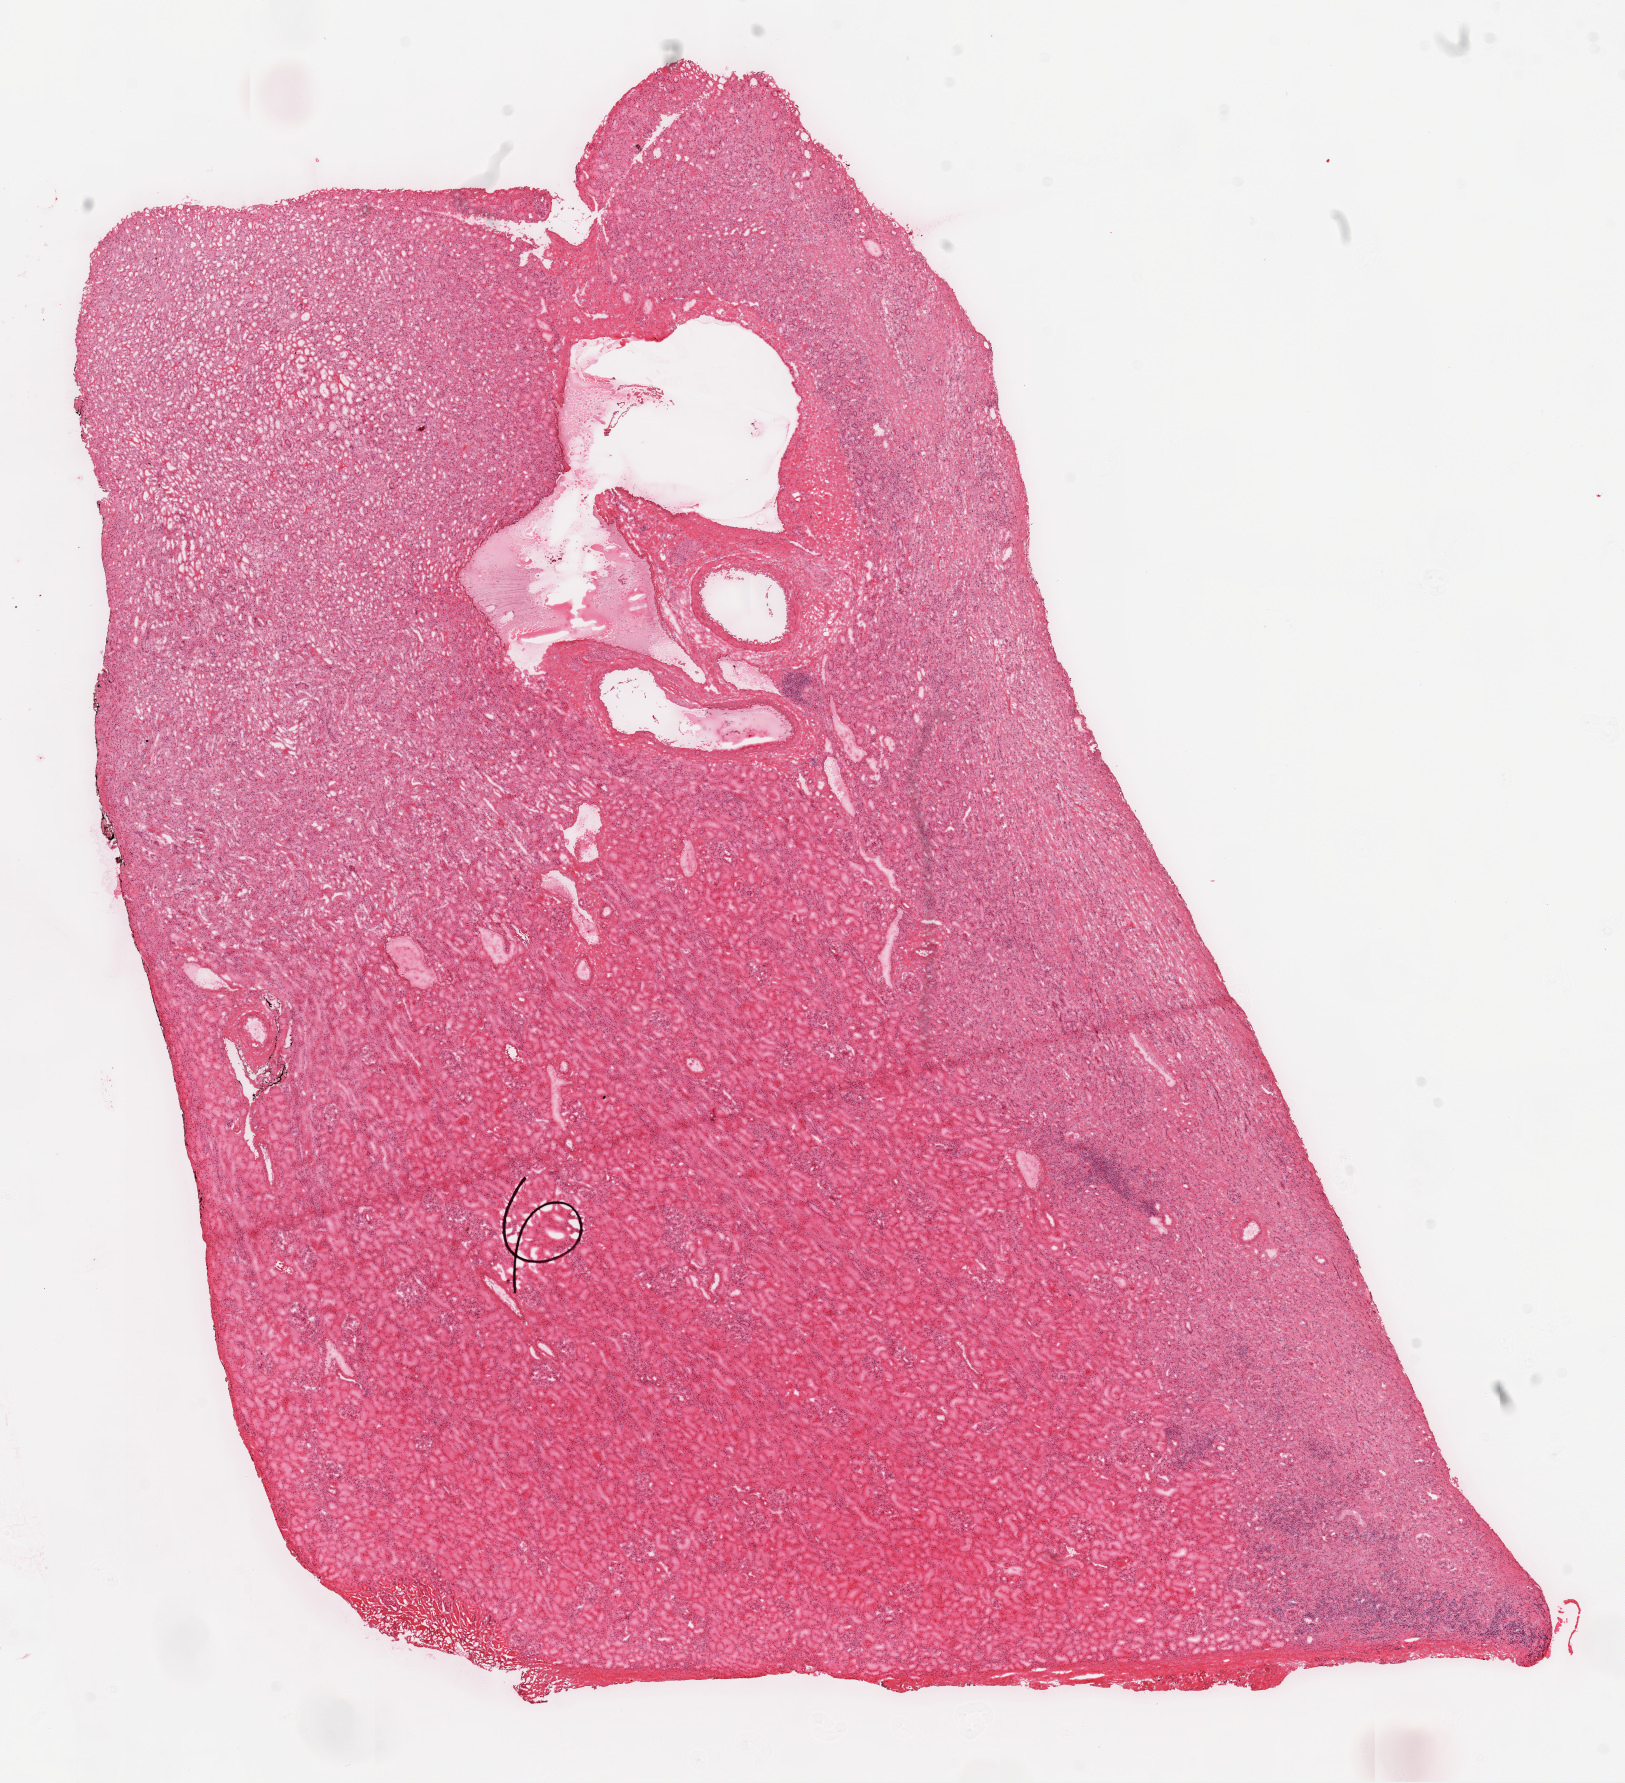
Whole-slide histology image, H&E — whole scanned area (about 13.0 x 14.3 mm, slide scanned at 20x) shown as a low-resolution overview, frozen section from the top of the tissue portion, kidney, solid tissue normal (non-tumour tissue) sample. Male patient; age at initial diagnosis 36 years.
This section: solid tissue normal (non-tumour) sample from the same patient. Patient diagnosis: Clear cell adenocarcinoma, NOS.